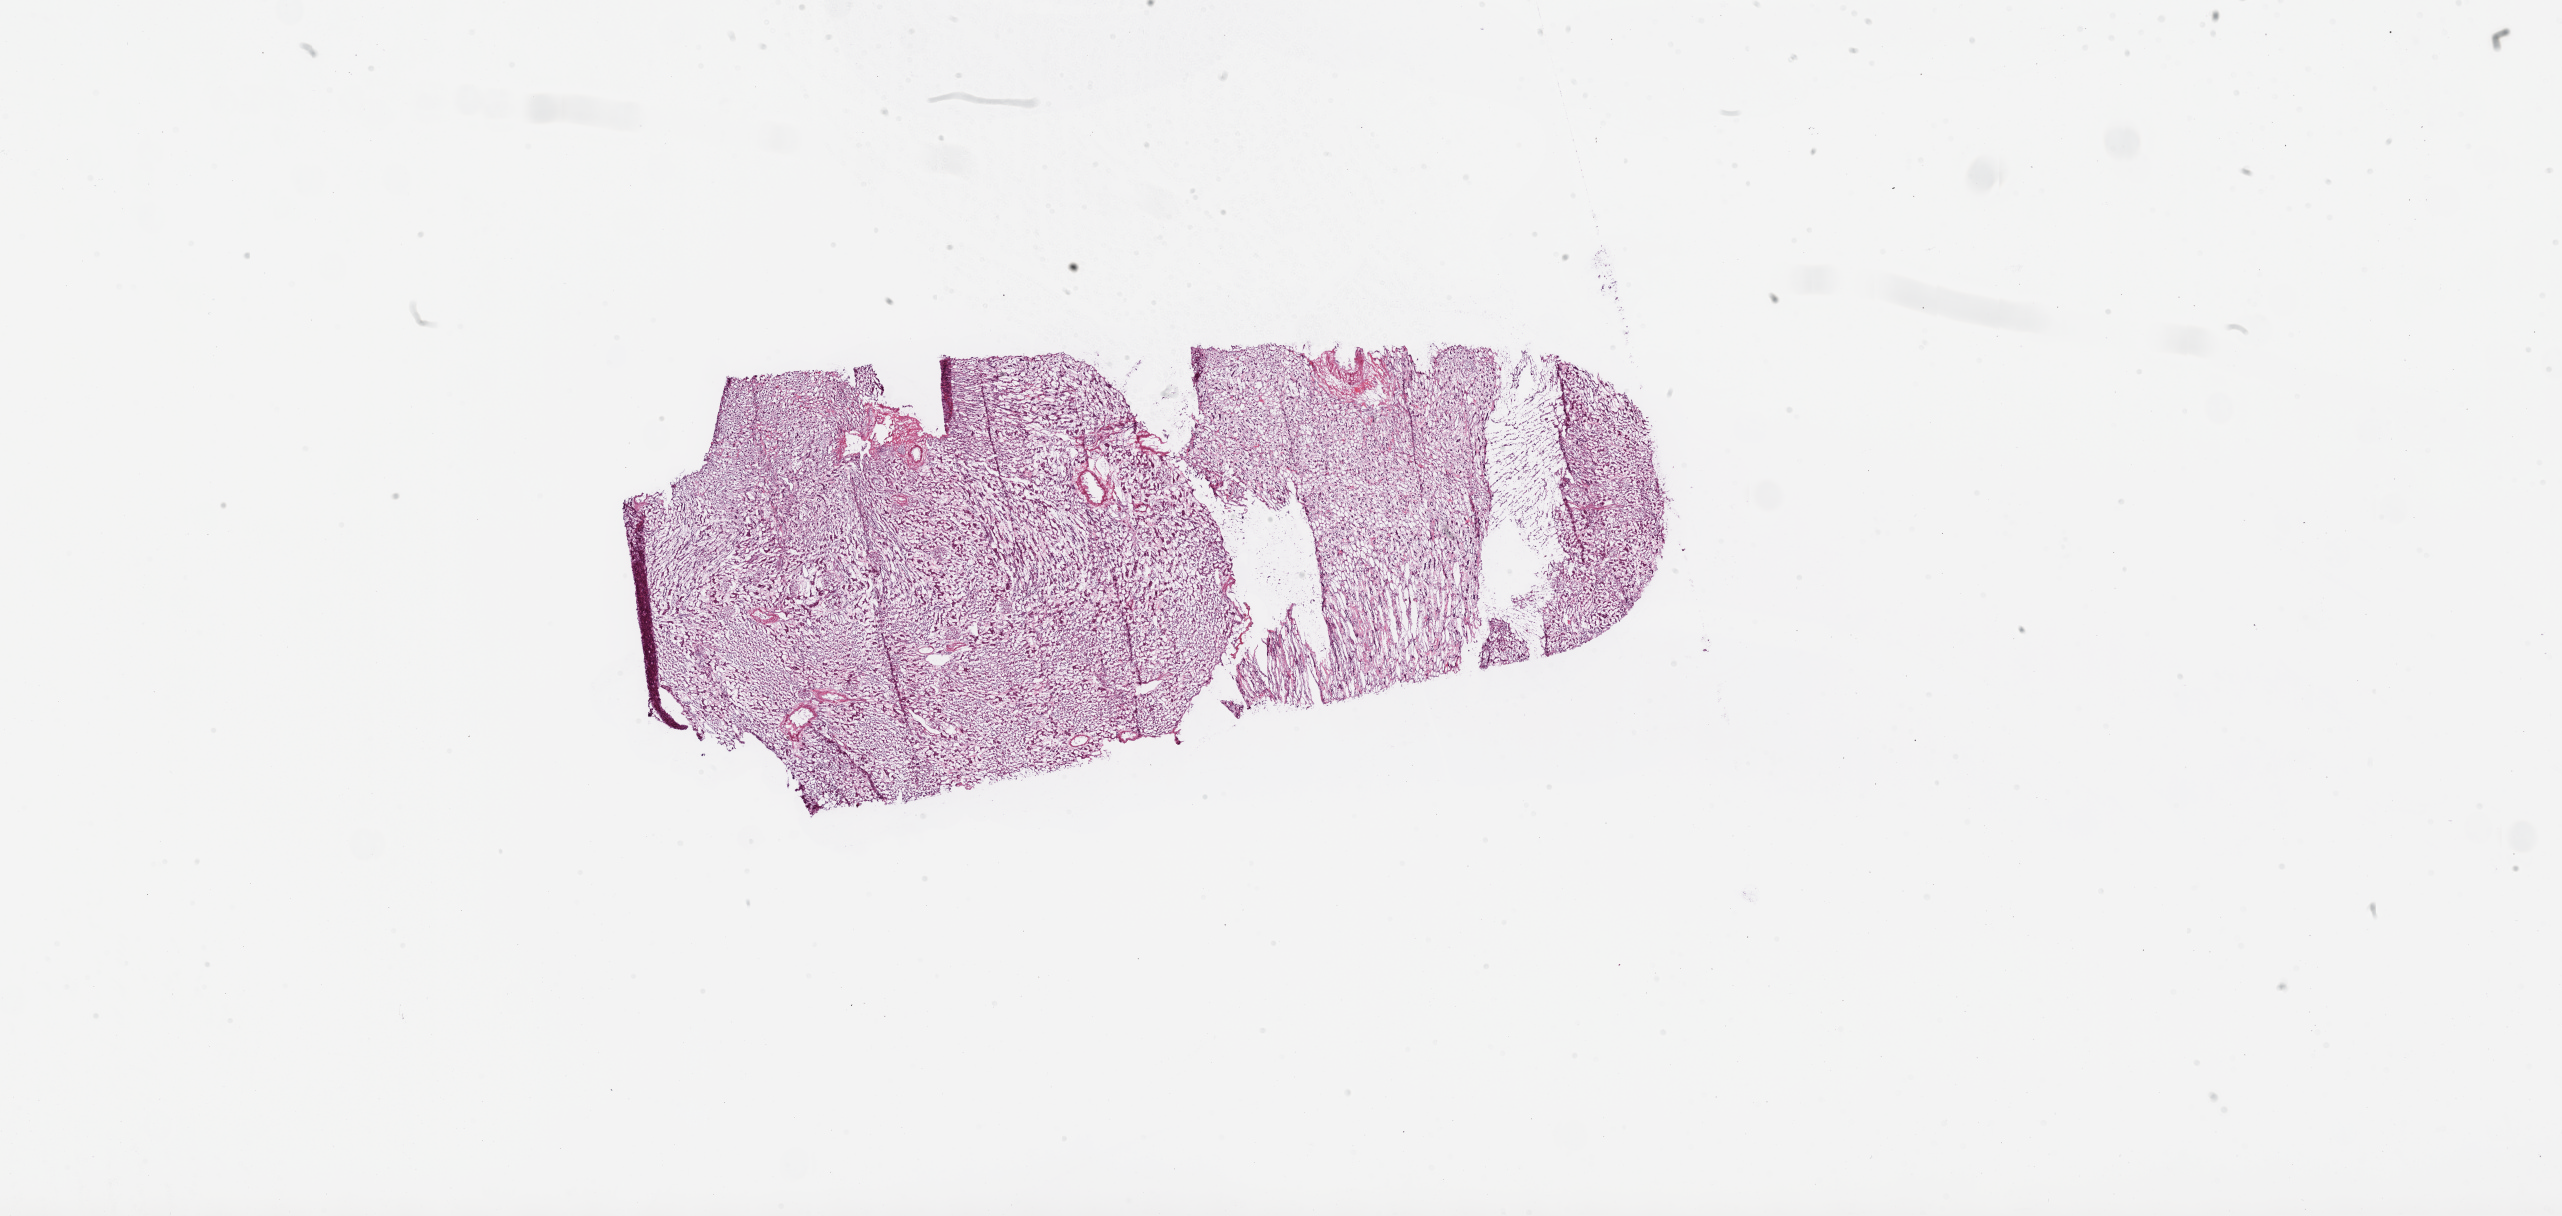
Whole-slide histology image, H&E — shown as a low-resolution overview of the whole scanned area (about 41.1 x 19.5 mm, acquisition: 20x scan); frozen section from the top of the tissue portion; sample: solid tissue normal (non-tumour tissue), kidney. Patient: female, age at initial diagnosis 34 years.
This section: solid tissue normal (non-tumour) sample from the same patient. Patient diagnosis: Clear cell adenocarcinoma, NOS.